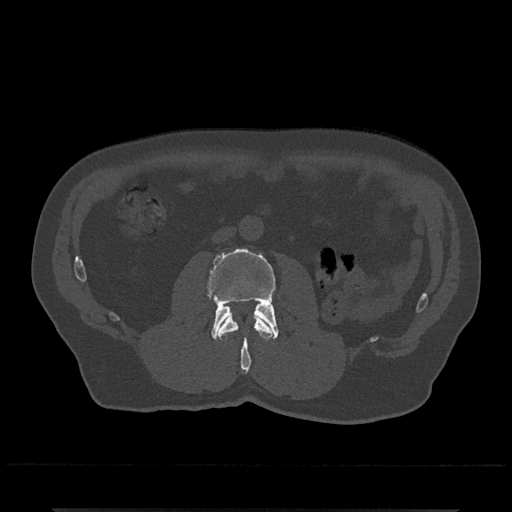
CT including the spine, one axial slice. Position 248 of 797 along the scan axis. Reconstruction kernel Br40s/3. Bone window (W 1800 / L 400 HU). 512 × 512 image matrix, field of view 393 × 393 mm. Male patient, age 67 years. Case-level facts recorded for this patient, not image findings: primary cancer: prostate.
Outlined on this slice (semi-automatically segmented with operator editing):
- L2 vertebra: bounding box [x1, y1, x2, y2] px = [218, 314, 273, 373]
- L3 vertebra: [207, 248, 278, 341]